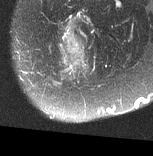
MRI of an extremity soft-tissue mass, one axial slice; position 19 of 77 along the scan axis; T2-weighted fat-saturated; MR volume resampled by the dataset authors to the PET/CT grid (not the native acquisition matrix); 3.27 mm slice thickness; 153 × 156 image matrix, field of view 149 × 152 mm. Female patient. Case-level facts recorded for this patient, not image findings: histological type: synovial sarcoma; grade: intermediate; site of the primary tumour: right buttock.
Annotated regions visible in this slice (expert contour drawn on MRI and transferred to this co-registered scan by the dataset authors):
- gross tumour volume including surrounding oedema: bounding box [x1, y1, x2, y2] px = [58, 22, 88, 76]
- gross tumour volume (mass): [64, 40, 82, 55]